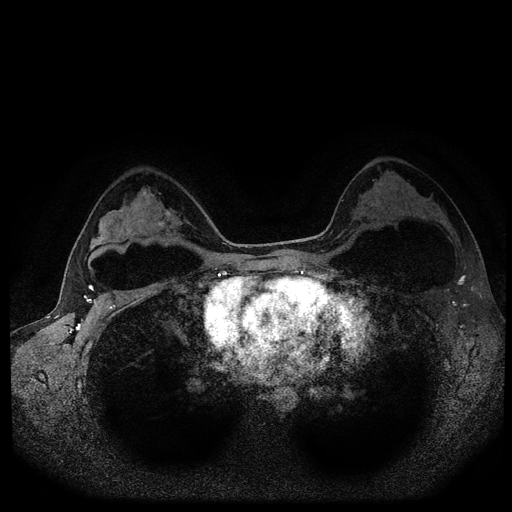
Breast MRI (dynamic contrast-enhanced, multi-phase), one axial slice. Slice 68 of 116 in the series (ordered by position). Dynamic contrast-enhanced series, time point 2 of 5 at this slice position (early post-contrast). 1.5 T. TE 2.6 ms, TR 5.4 ms. 2 mm slice thickness. 512 × 512 image matrix, field of view 340 × 340 mm. Patient: female, 33 years.
Annotated regions visible in this slice (semi-automatically segmented with operator editing):
- breast lesion (labelled benign in the annotation): bounding box [x1, y1, x2, y2] px = [158, 209, 173, 227]
- breast lesion (labelled benign in the annotation): [143, 189, 155, 200]